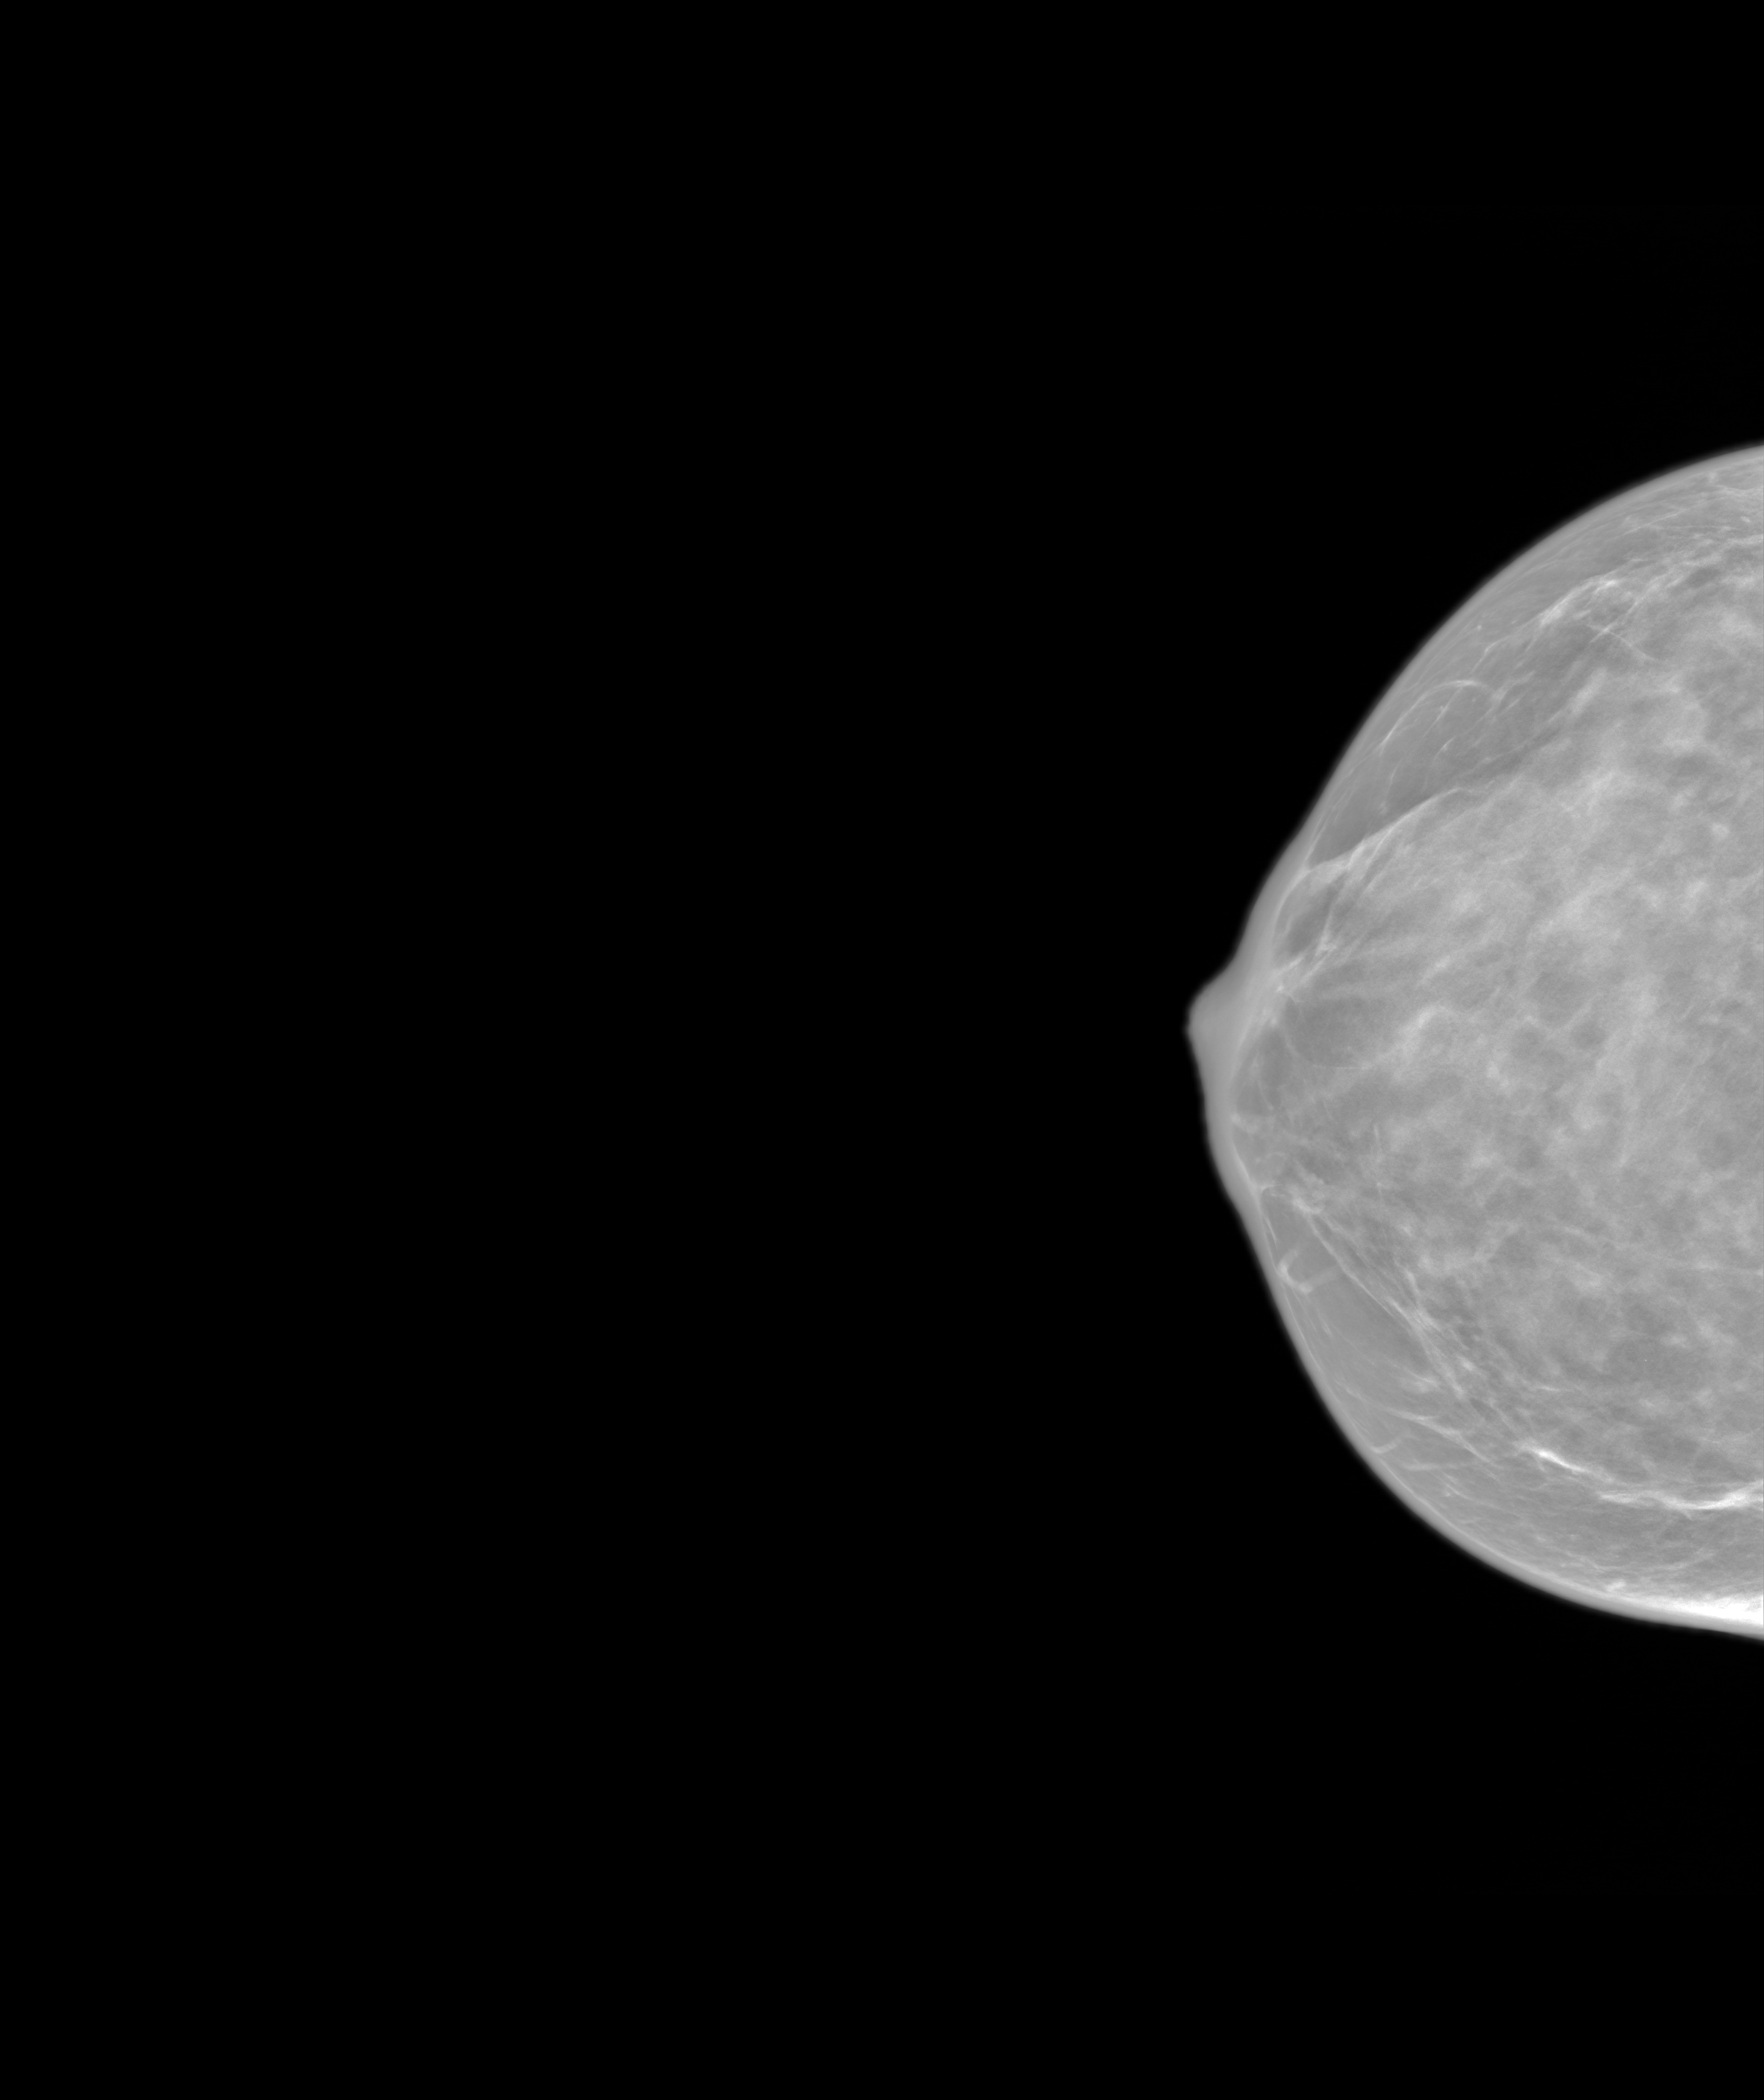
Screening examination. Patient aged 43 years (female).
Image type: synthesized 2-D view from tomosynthesis. Breast: right. Projection: craniocaudal (CC) view.